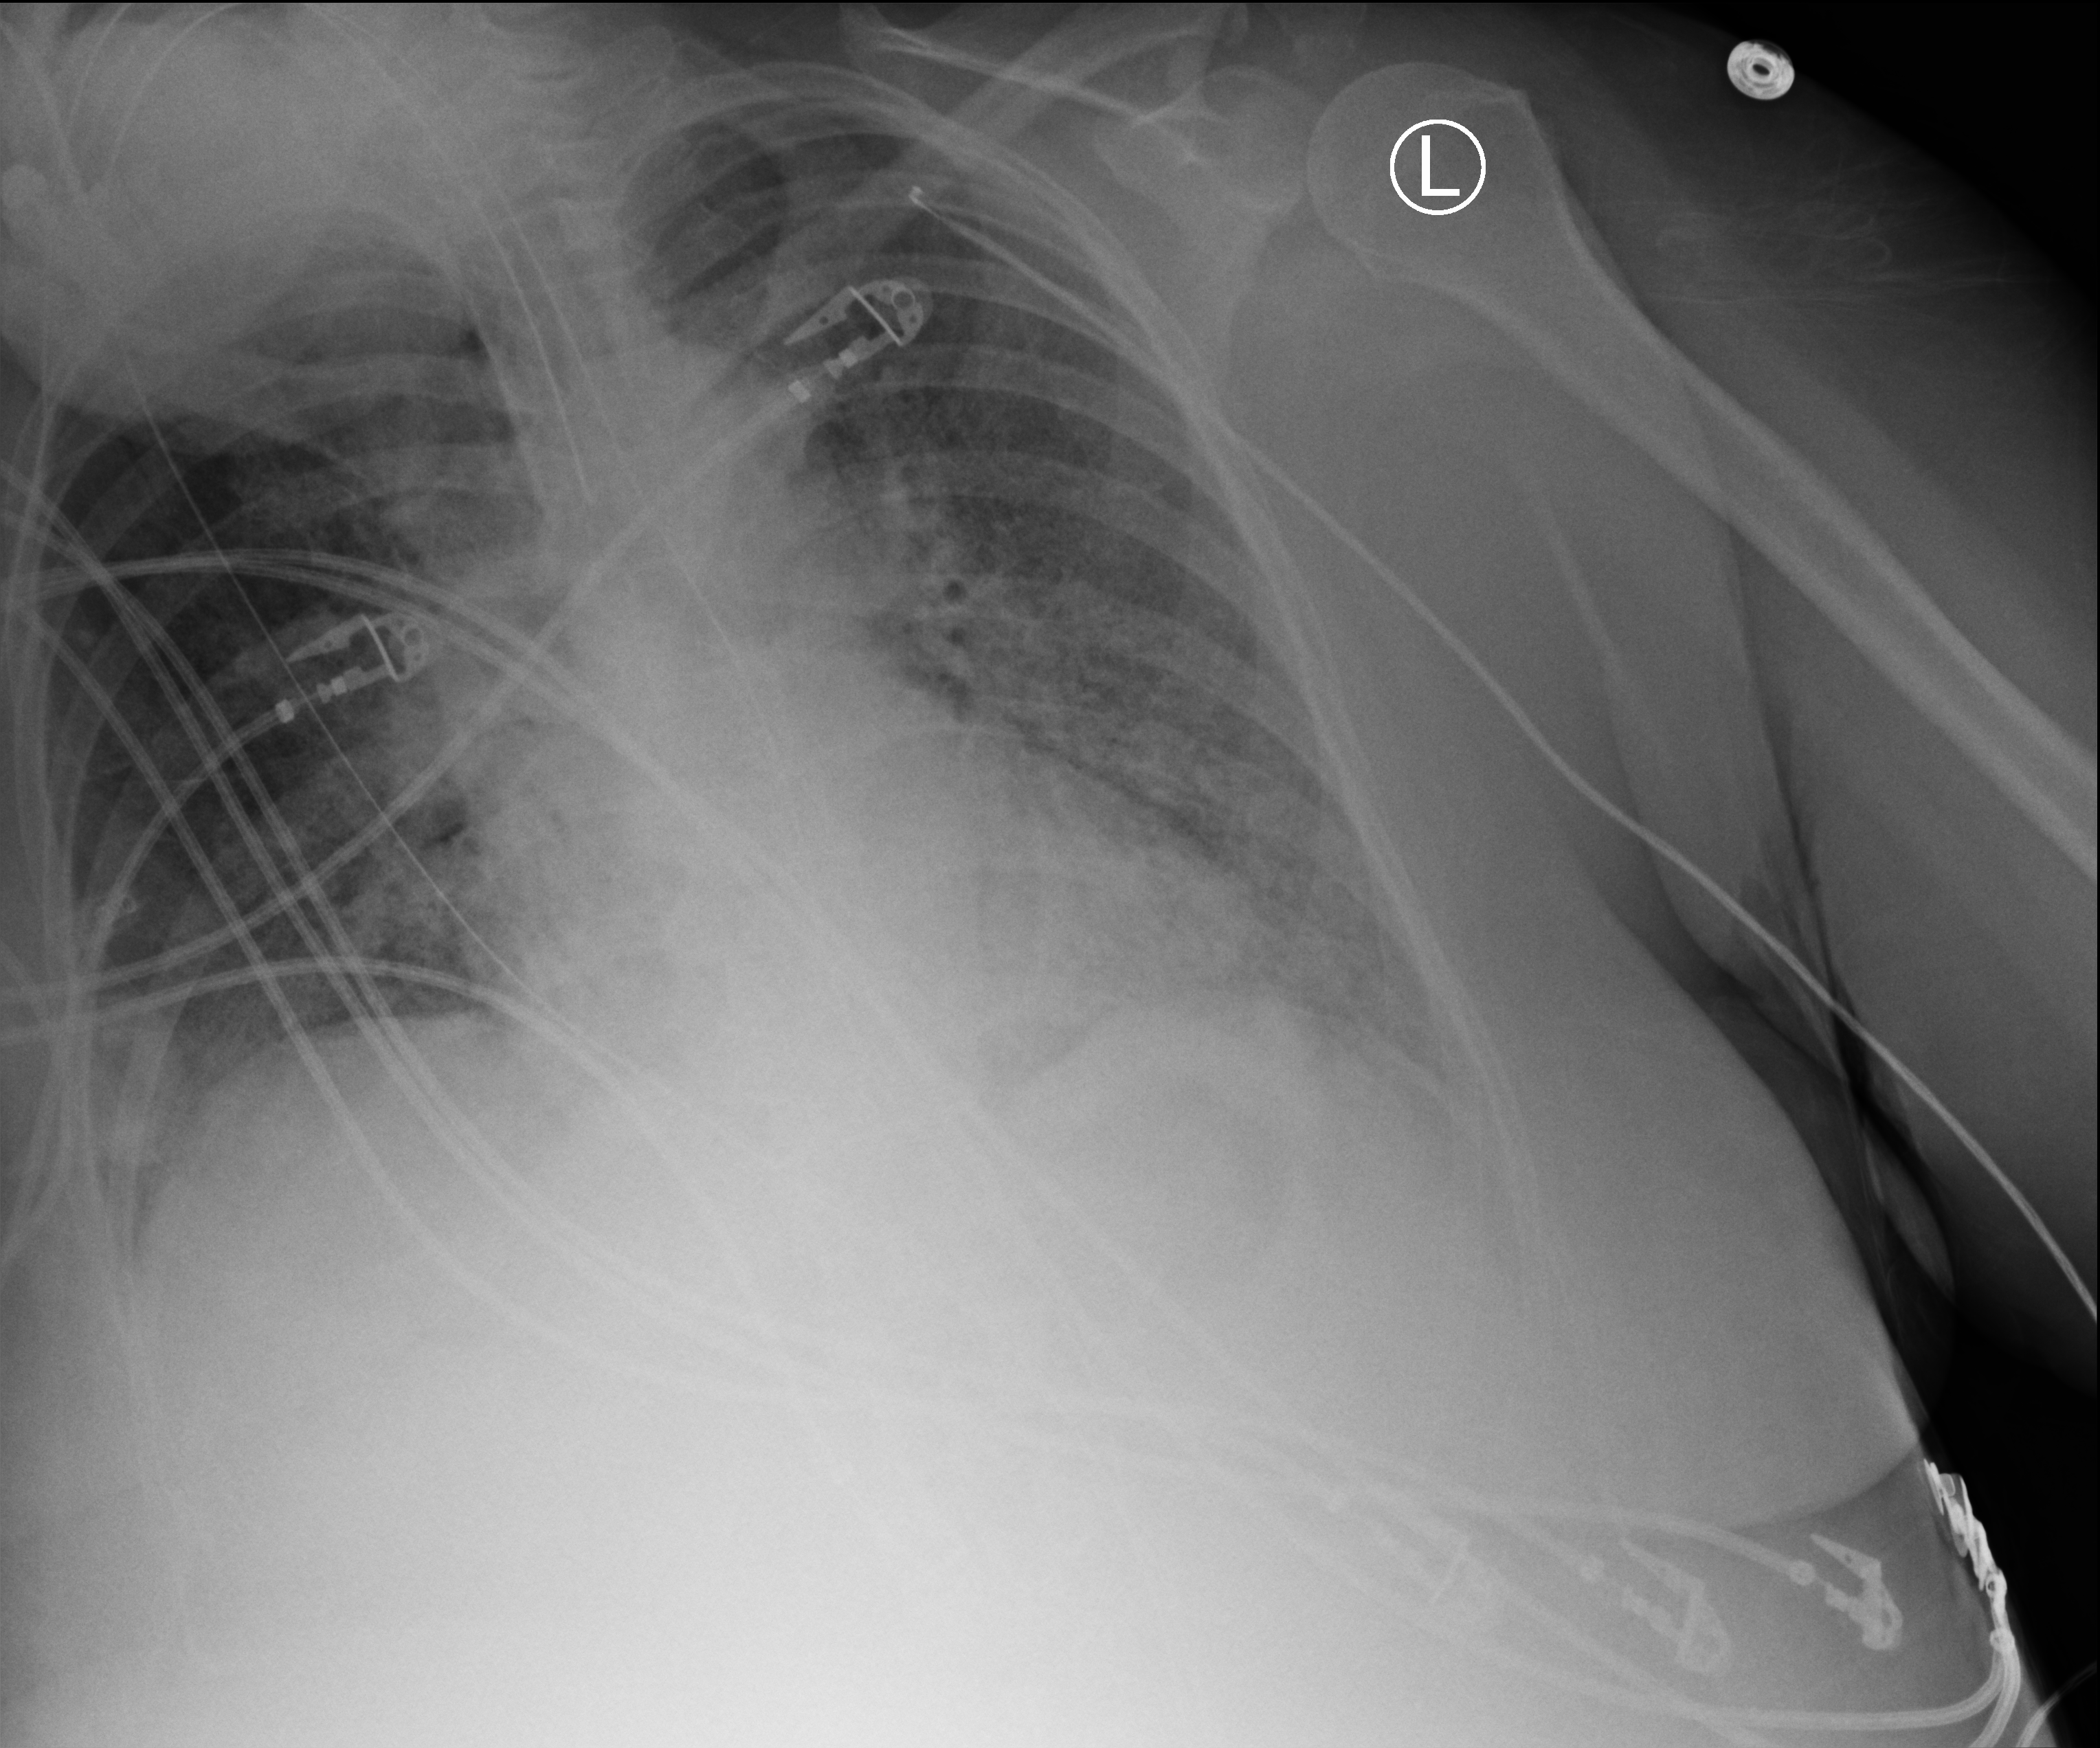
Bedside chest radiograph (computed radiography). Female patient hospitalised with COVID-19, age 60–74 years.
Admission-level facts for this patient (not findings on this image; timing relative to this image not recorded): mechanically ventilated during this hospital stay: yes.